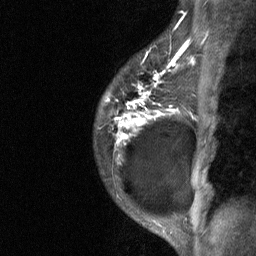
Breast MRI (dynamic contrast-enhanced), one sagittal slice. Slice 50 of 64 in the series (ordered by position). Dynamic contrast-enhanced study with each time point stored as its own series, time point 2 of 3 at this slice position (early post-contrast, ordered by acquisition time). 1.5 T. TE 4.8 ms, TR 27 ms. 2 mm slice thickness. 256 × 256 image matrix. Female patient, age 34 years. Case-level facts recorded for this patient, not image findings: setting: breast cancer imaged before/during neoadjuvant chemotherapy; receptor status: HR-positive, HER2-negative.
Annotated regions visible in this slice (semi-automatic segmentation, software-assisted and operator-edited):
- analysis volume of interest (the breast-tissue region the enhancement analysis was run in; not a lesion): box from (x=94, y=44) to (x=181, y=191) px
- tumour enhancement mask (voxels above the 90 % enhancement threshold inside the analysis volume of interest): (x=114, y=49)–(x=181, y=144)